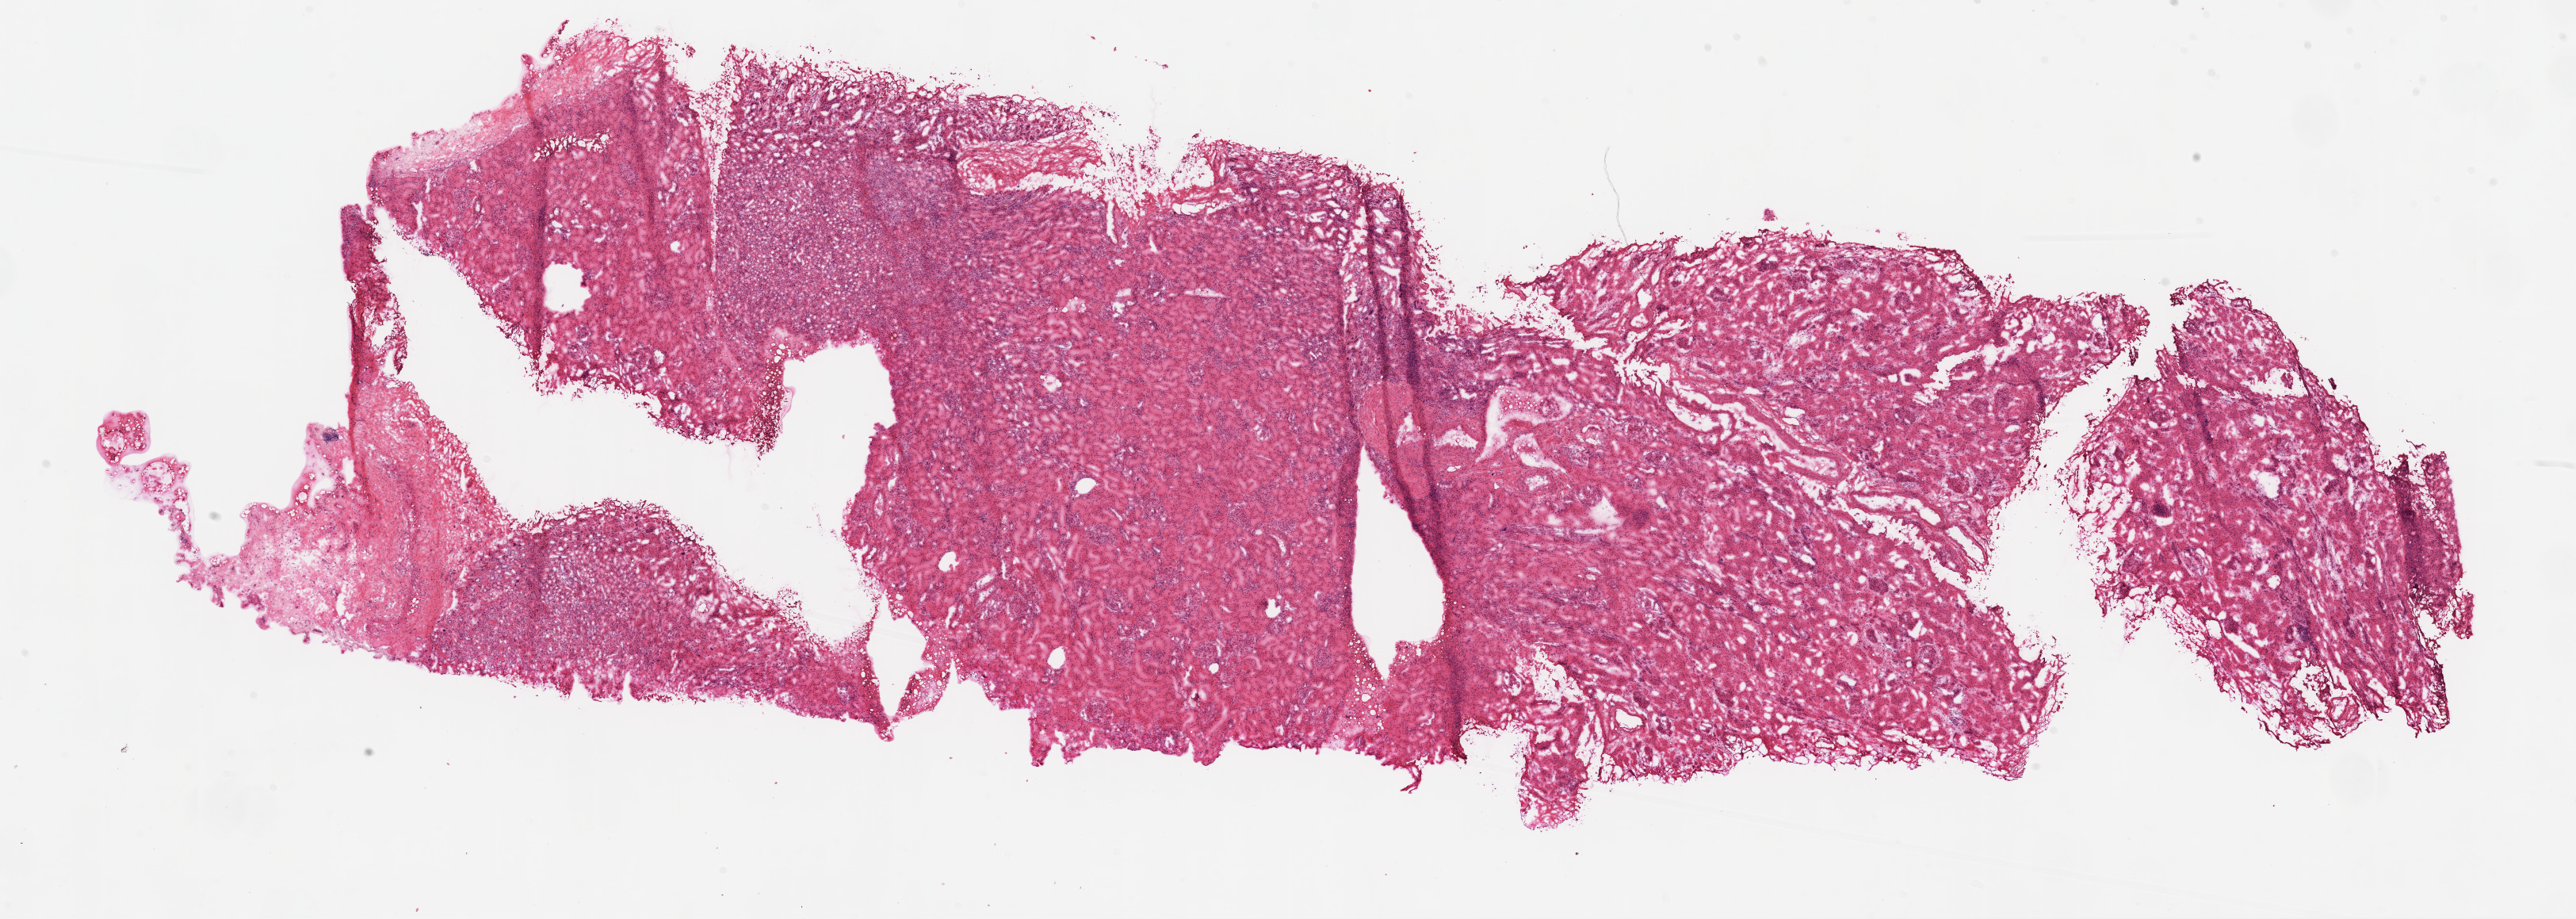
Digitized H&E-stained tissue section (whole slide) — shown as a low-resolution overview of the whole scanned area (about 26.1 x 9.3 mm, slide scanned at 20x), frozen section, kidney, solid tissue normal (non-tumour tissue) sample. Patient: male, age at initial diagnosis 67 years.
This section: solid tissue normal sample (biorepository sample class). Patient diagnosis: Clear cell adenocarcinoma, NOS.